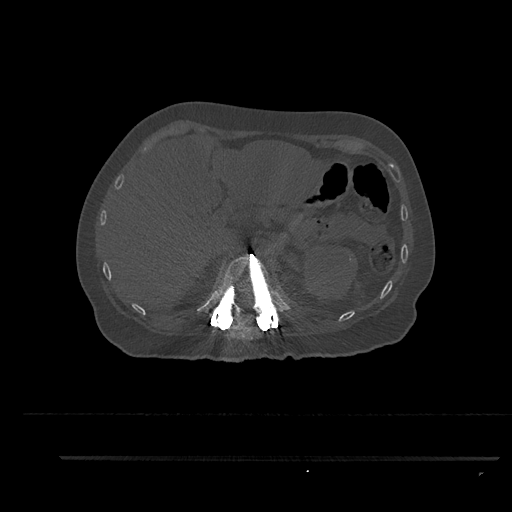
CT including the spine, one axial slice. Slice 271 of 797 in the series (ordered by position). Reconstruction kernel Br40s/3. 120 kVp. Bone window (W 1800 / L 400 HU). 512 × 512 image matrix. Female patient, age 44 years. Case-level facts recorded for this patient, not image findings: primary cancer: renal.
Annotated regions visible in this slice (semi-automatic segmentation, software-assisted and operator-edited):
- T12 vertebra: bounding box [x1, y1, x2, y2] px = [213, 253, 283, 320]